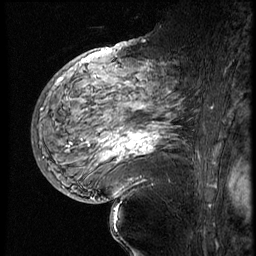
Breast MRI (dynamic contrast-enhanced), one sagittal slice. Position 36 of 60 along the scan axis. 4 images stored at this slice position (order not interpretable as contrast timing). 1.5 T. TE 4.2 ms, TR 9 ms. 2.5 mm slice thickness. 256 × 256 image matrix, field of view 180 × 180 mm. Patient: female, 56 years. Case-level facts recorded for this patient, not image findings: setting: breast cancer imaged before/during neoadjuvant chemotherapy; receptor status: HER2-positive.
Outlined on this slice (semi-automatically segmented with operator editing):
- analysis volume of interest (the breast-tissue region the enhancement analysis was run in; not a lesion): box from (x=82, y=83) to (x=199, y=177) px
- tumour enhancement mask (voxels above the 140 % enhancement threshold inside the analysis volume of interest): (x=103, y=125)–(x=163, y=162)